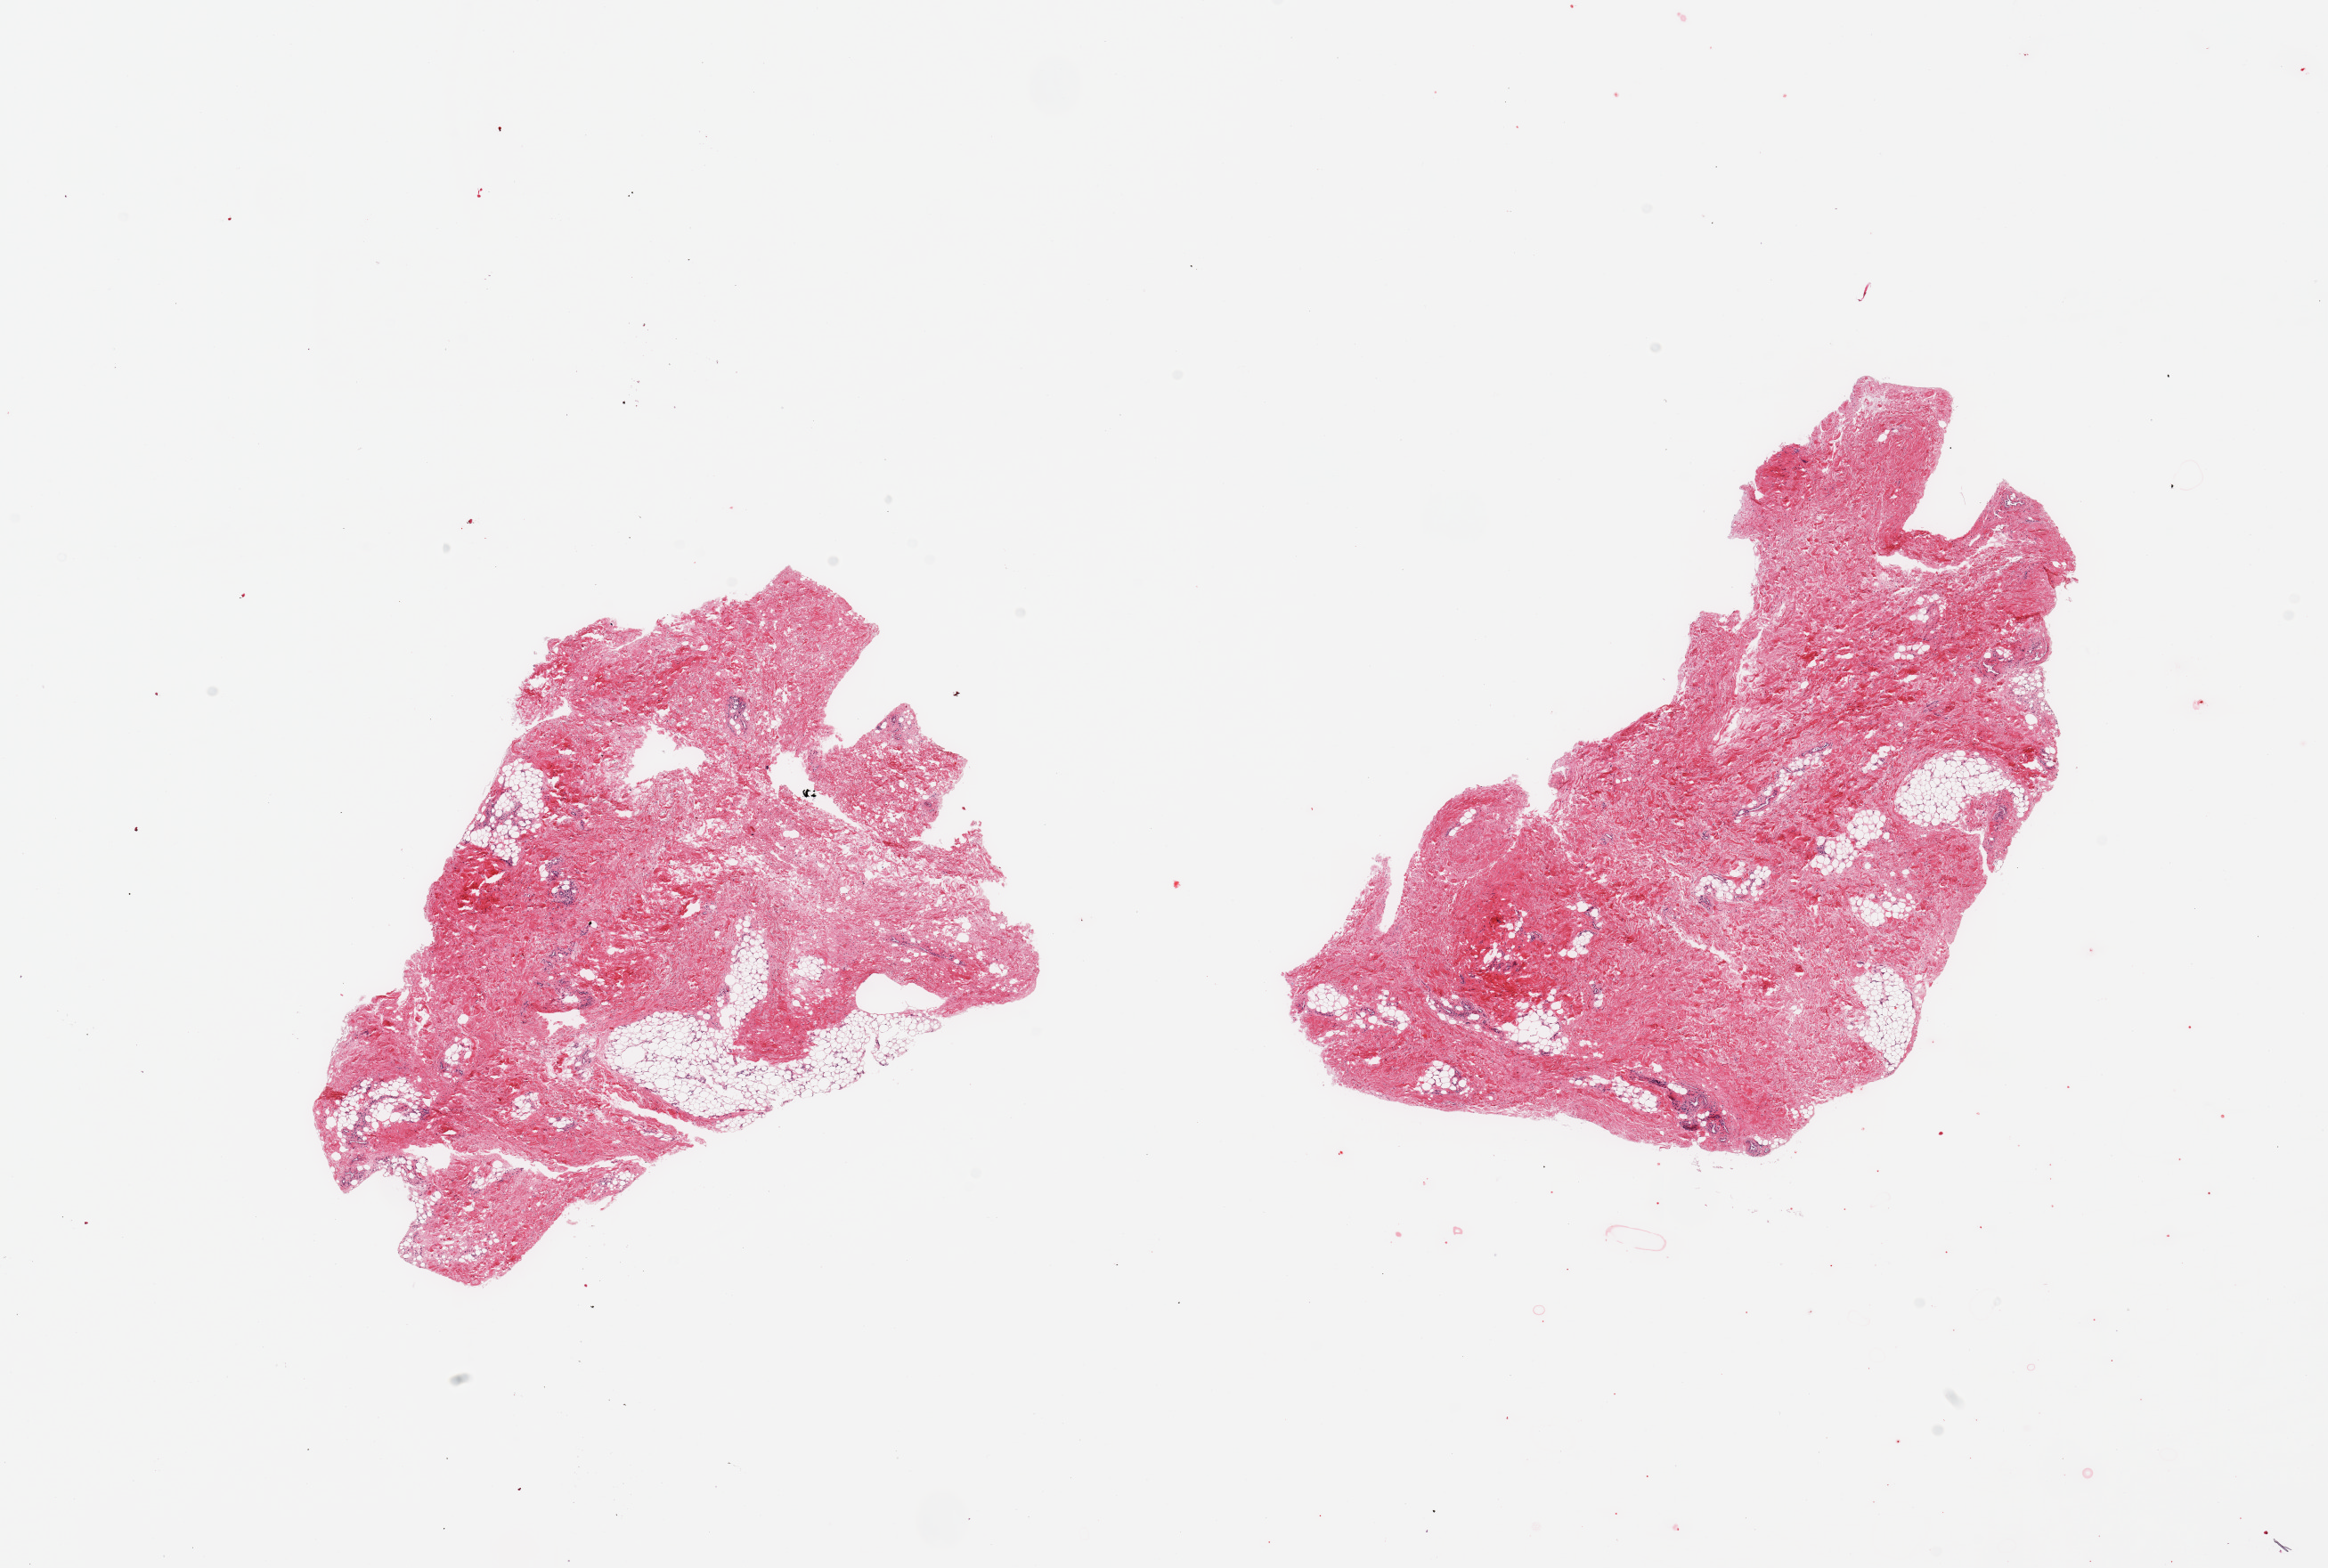
Whole-slide image, H&E stain — whole scanned area (about 20.7 x 13.9 mm) shown as a low-resolution overview, PAXgene-fixed, paraffin-embedded tissue, sampled site (target tissue): breast, tissue donor sample. Donor: male.
Review note (as recorded): 2 pieces; predominantly fibrovascular stroma with 20% and 10% adipose tissue.